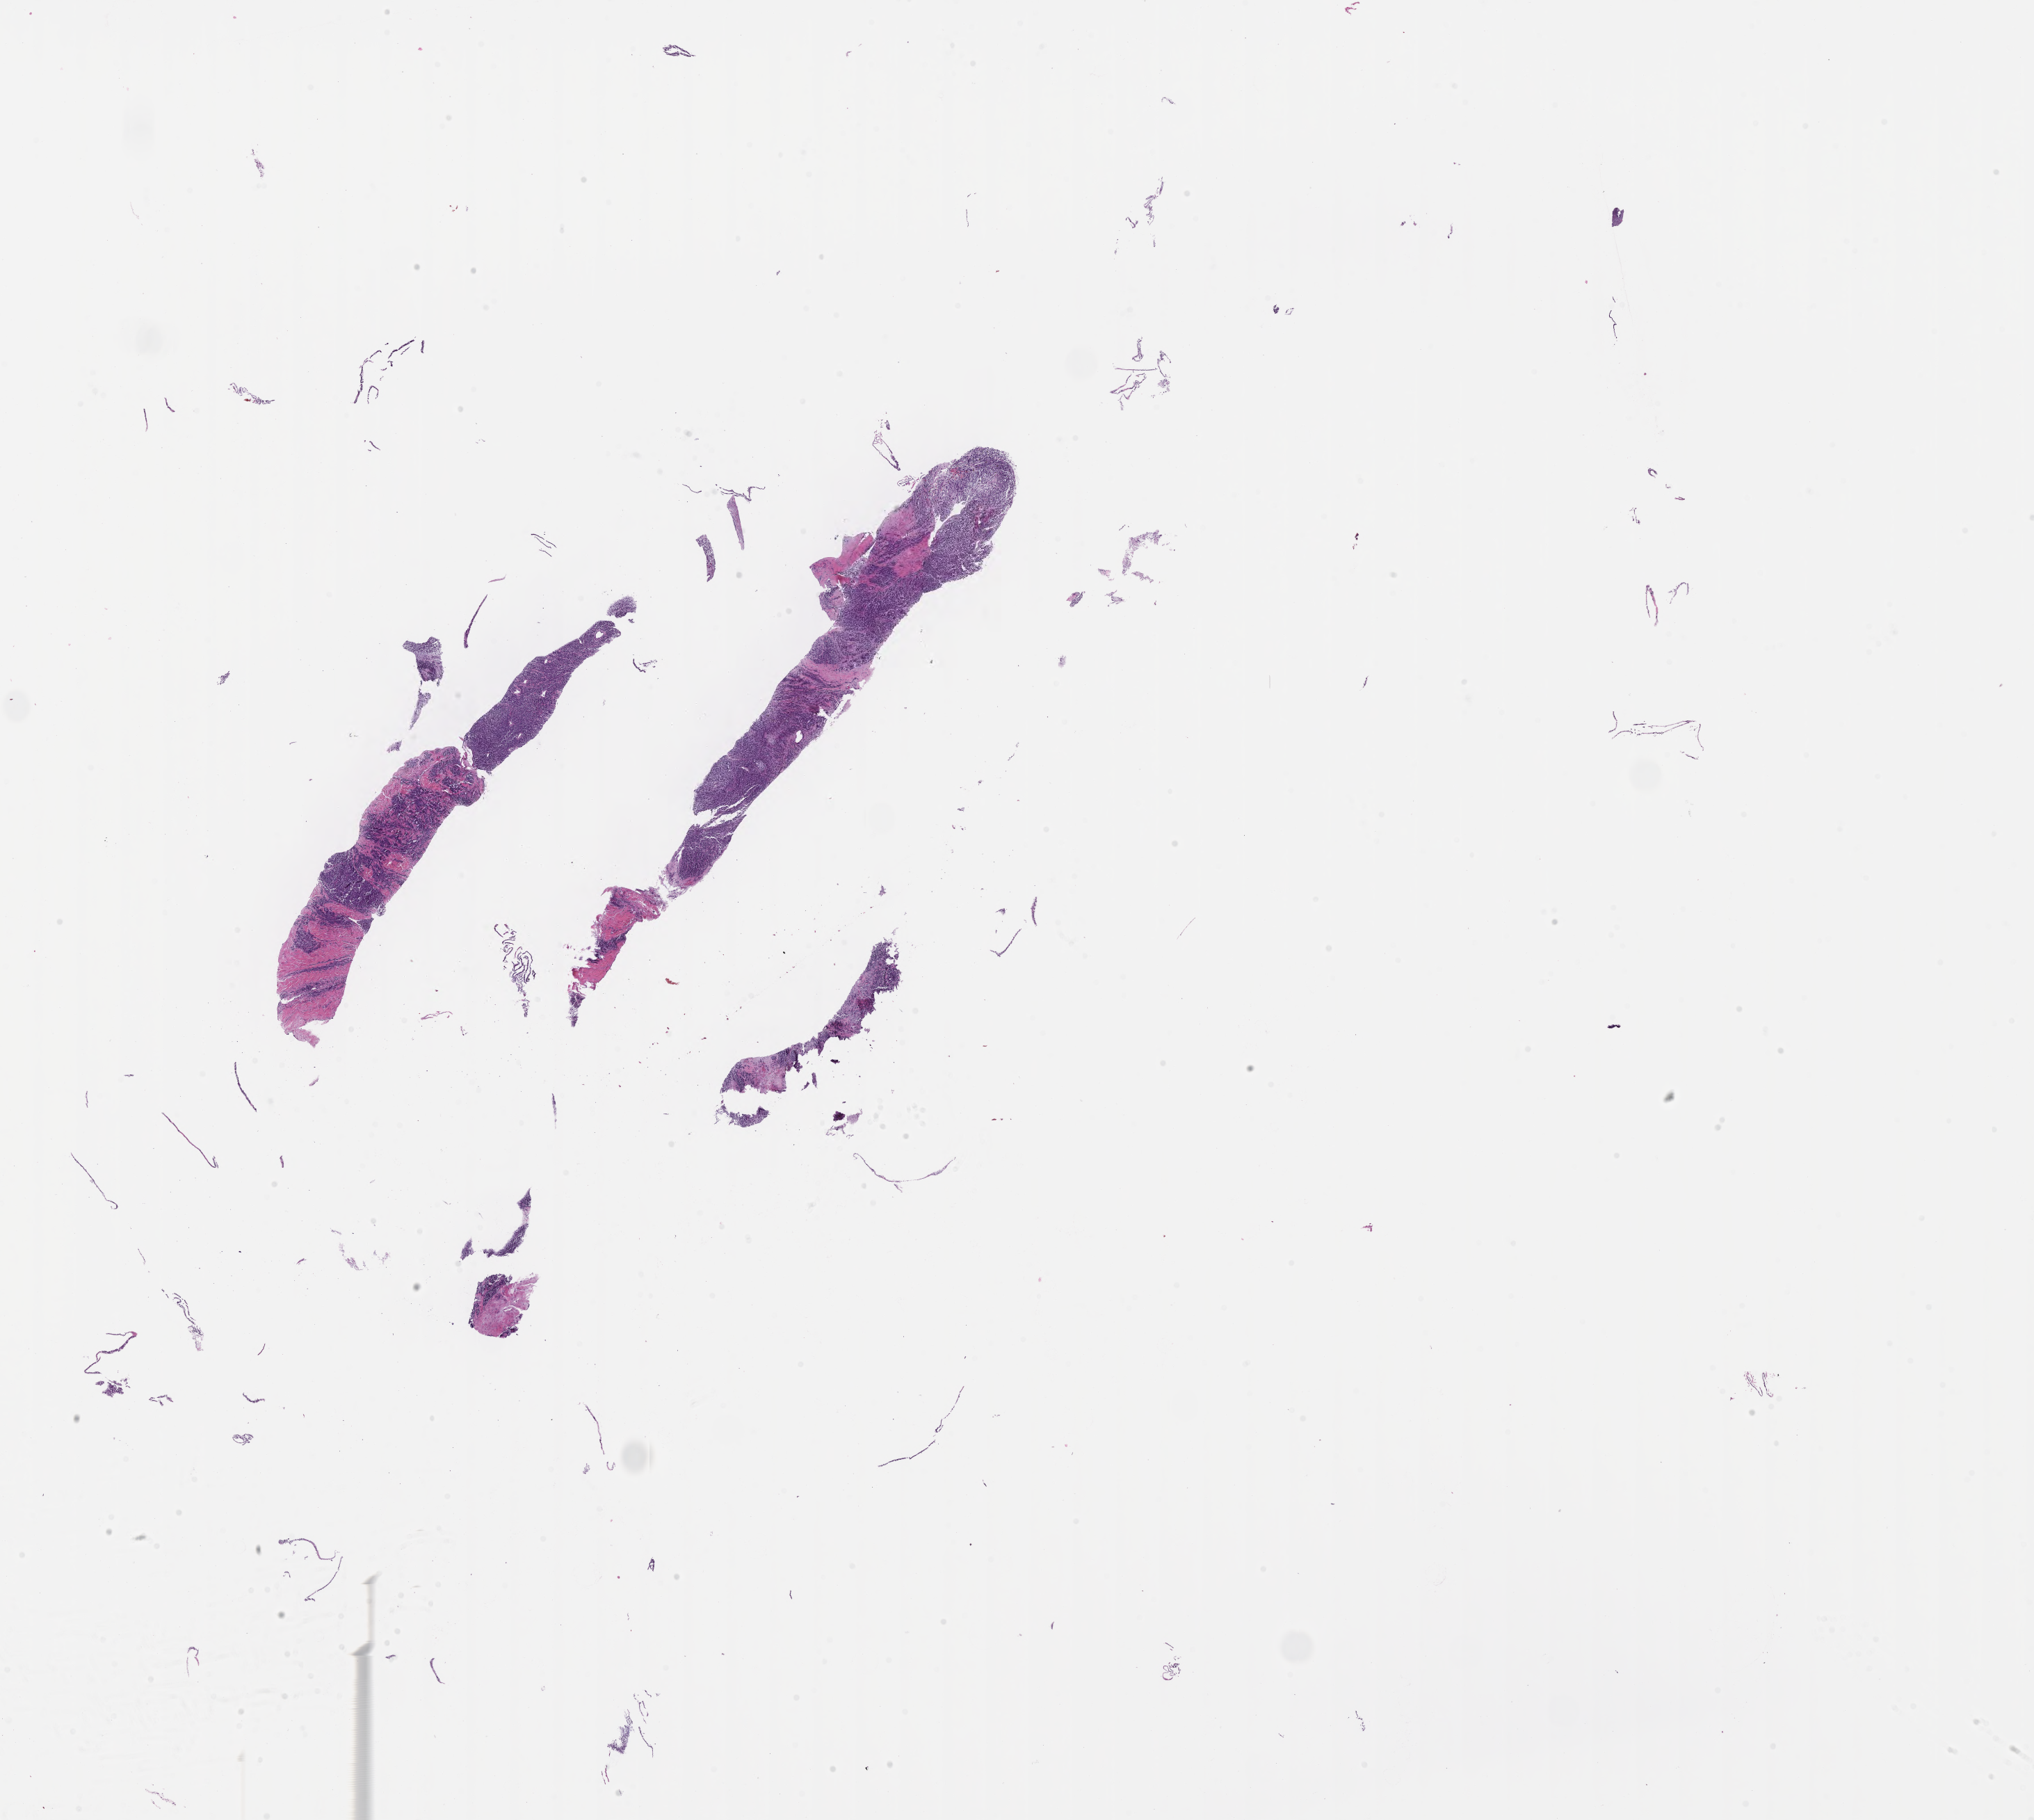
H&E whole-slide image of tumor tissue from the long bone of upper limb — shown as a low-resolution overview of the whole scanned area (about 23.6 x 21.2 mm); FFPE section. Male patient, age 209 months (17 years 5 months).
Diagnosis: Clear cell sarcoma, NOS.